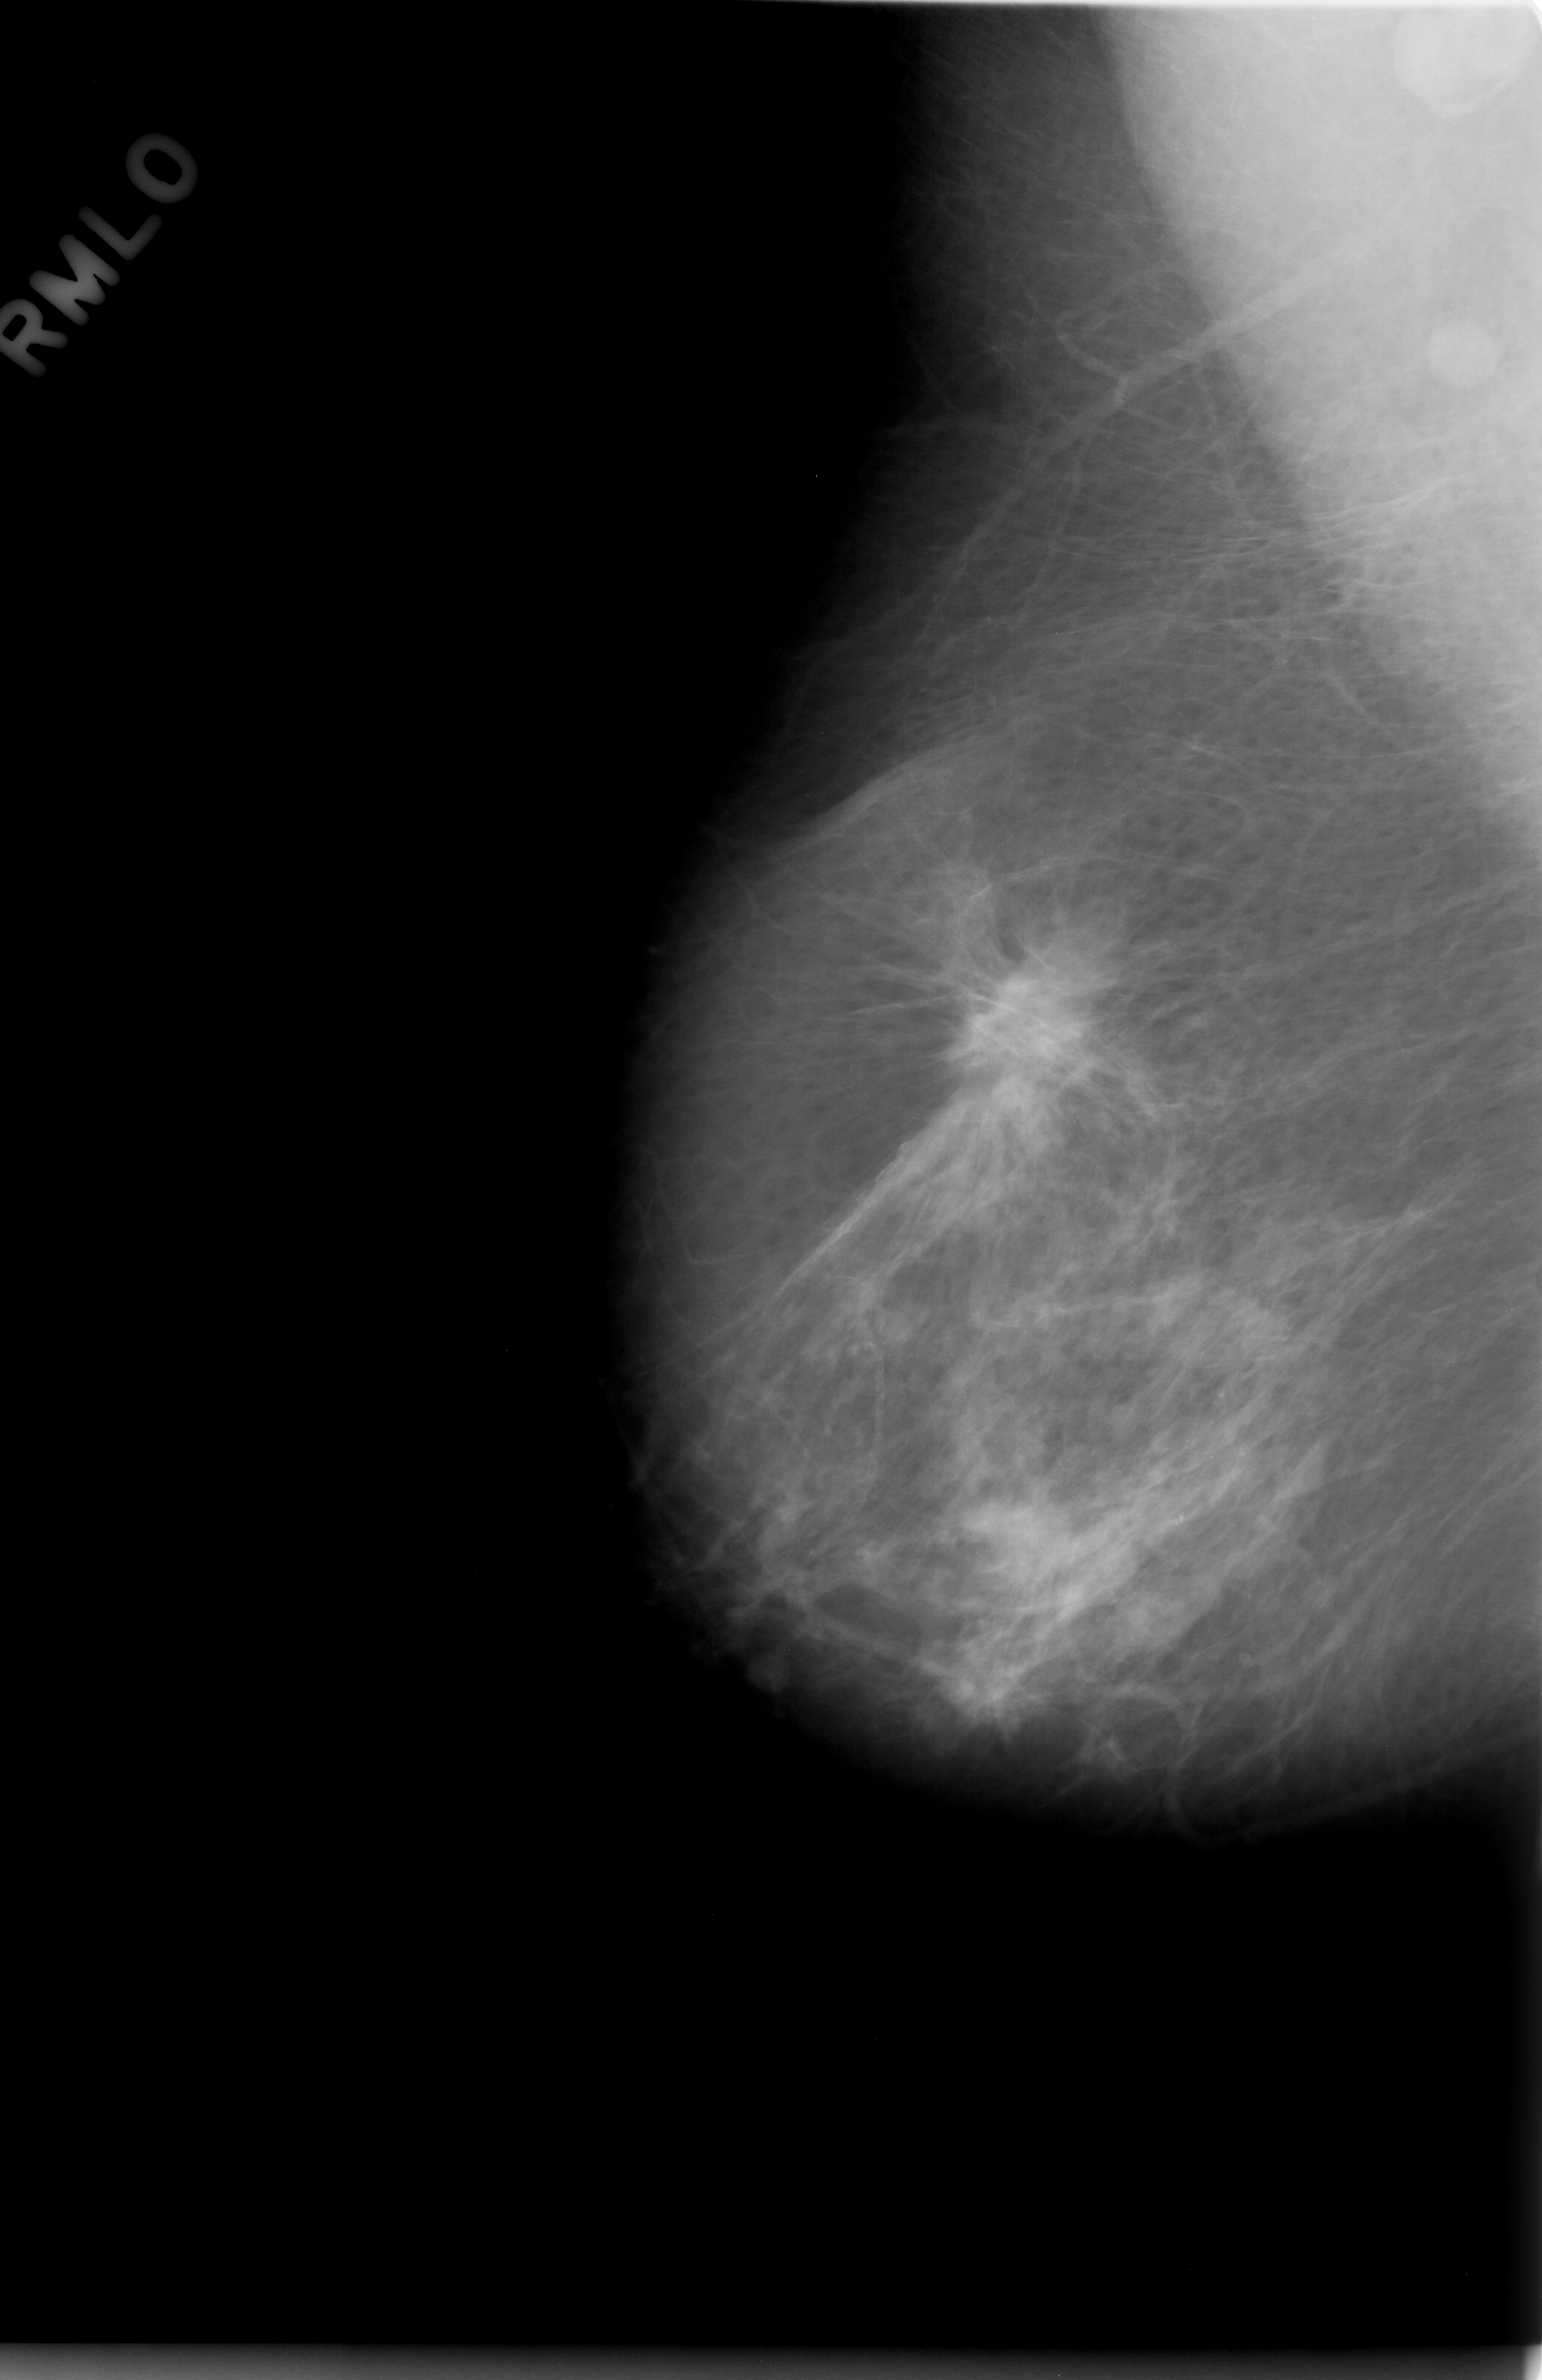
Mammogram (digitized film); right breast; MLO view; BI-RADS breast density category 2 (scale 1–4); 1542 × 2380 image matrix.
Expert-marked regions of interest on this image (one box per marked abnormality):
- mass, shape architectural distortion, margins spiculated; BI-RADS assessment category 2; pathology result (as recorded, not read from the image): benign: box from (x=927, y=963) to (x=1114, y=1172) px